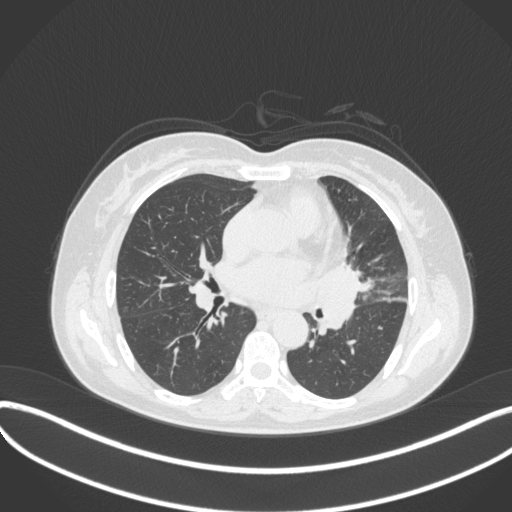
Chest CT, one axial slice. 120 kVp. Lung window (W 1500 / L -600 HU). 512 × 512 image matrix. Patient: female, 54 years. Case-level facts recorded for this patient, not image findings: clinical TNM (as recorded): T2a N1 M0; histopathological grade: G3.
Outlined on this slice (bounding box drawn by a radiologist):
- lung tumour (recorded histology: small cell carcinoma): bounding box (x1, y1, x2, y2) in pixels: (311, 261, 369, 340)